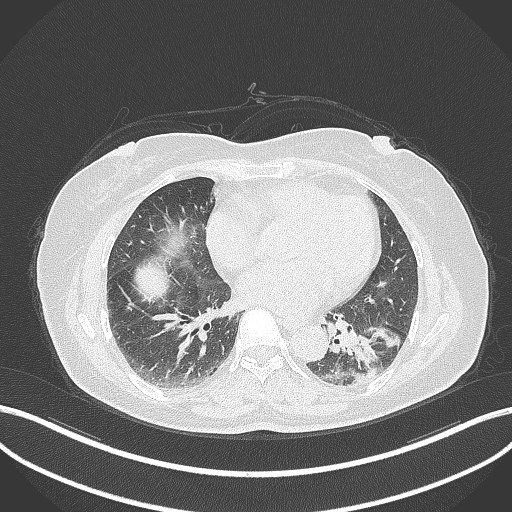
Chest CT, one axial slice; position 158 of 311 along the scan axis; reconstruction kernel B70f; lung window (W 1500 / L -600 HU); 1 mm slice thickness; 512 × 512 image matrix. Female patient, age 59 years. From the clinical record (not read from this slice): clinical TNM (as recorded): T2a N0 M0; histopathological grade: G2-3.
Outlined on this slice (bounding box drawn by a radiologist):
- lung tumour (recorded histology: adenocarcinoma): bounding box (x1, y1, x2, y2) in pixels: (338, 321, 401, 382)